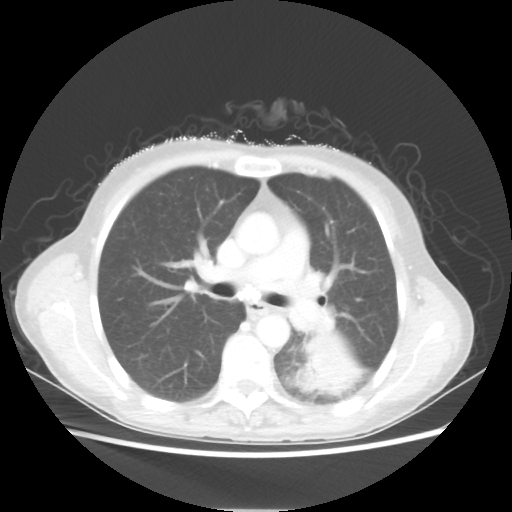
Chest CT, one axial slice; position 34 of 56 along the scan axis; reconstruction kernel STANDARD; lung window (W 1500 / L -600 HU); 512 × 512 image matrix, field of view 360 × 360 mm. Female patient, age 53 years. From the clinical record (not read from this slice): clinical TNM (as recorded): T3 N0 M0.
Structures marked on this image (bounding box drawn by a radiologist):
- lung tumour (recorded histology: adenocarcinoma): bounding box [x1, y1, x2, y2] px = [298, 333, 363, 395]